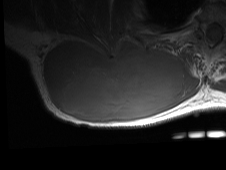
MRI of an extremity soft-tissue mass, one axial slice. Position 40 of 81 along the scan axis. MR volume resampled by the dataset authors to the PET/CT grid (not the native acquisition matrix). 3.27 mm slice thickness. 226 × 170 image matrix. Male patient. Case-level facts recorded for this patient, not image findings: histological type: pleiomorphic spindle cell undifferentiated; grade: high; site of the primary tumour: right parascapusular.
Annotated regions visible in this slice (expert contour drawn on MRI and transferred to this co-registered scan by the dataset authors):
- gross tumour volume including surrounding oedema: bounding box [x1, y1, x2, y2] px = [42, 38, 198, 123]
- gross tumour volume (mass): [42, 40, 184, 123]